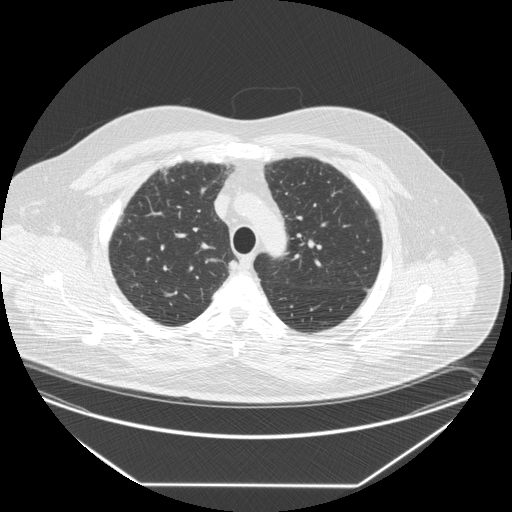
Low-dose screening chest CT, one axial slice. Slice 207 of 258 in the series (ordered by position). Reconstruction kernel STANDARD. 120 kVp. Lung window (W 1500 / L -600 HU). 512 × 512 image matrix, field of view 440 × 440 mm.
Outlined on this slice (outlined manually by an expert reader):
- lesion 1 (tumor, upper lobe of right lung): bounding box (x1, y1, x2, y2) in pixels: (229, 260, 238, 273)